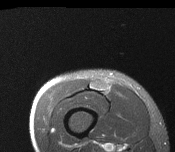
MRI of an extremity soft-tissue mass, one axial slice; slice 29 of 116 in the series (ordered by position); T2-weighted fat-saturated; MR volume resampled by the dataset authors to the PET/CT grid (not the native acquisition matrix); 3.27 mm slice thickness; 175 × 152 image matrix. Male patient. Case-level facts recorded for this patient, not image findings: histological type: pleiomorphic leiomyosarcoma; grade: intermediate; site of the primary tumour: right thigh.
Annotated regions visible in this slice (expert contour drawn on MRI and transferred to this co-registered scan by the dataset authors):
- gross tumour volume including surrounding oedema: bounding box [x1, y1, x2, y2] px = [92, 81, 107, 91]